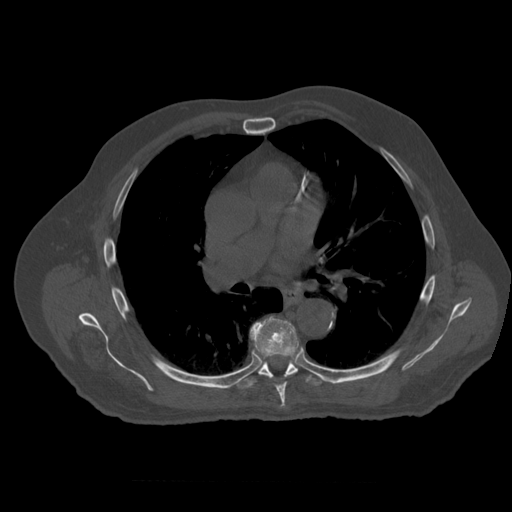
CT including the spine, one axial slice. Position 372 of 399 along the scan axis. Reconstruction kernel STANDARD. Bone window (W 1800 / L 400 HU). 1.25 mm slice thickness. 512 × 512 image matrix, field of view 407 × 407 mm. Patient age 73 years. Case-level facts recorded for this patient, not image findings: primary cancer: prostate.
Outlined on this slice (semi-automatically segmented with operator editing):
- T6 vertebra: box from (x=250, y=317) to (x=299, y=409) px
- T7 vertebra: (x=237, y=346)–(x=326, y=389)